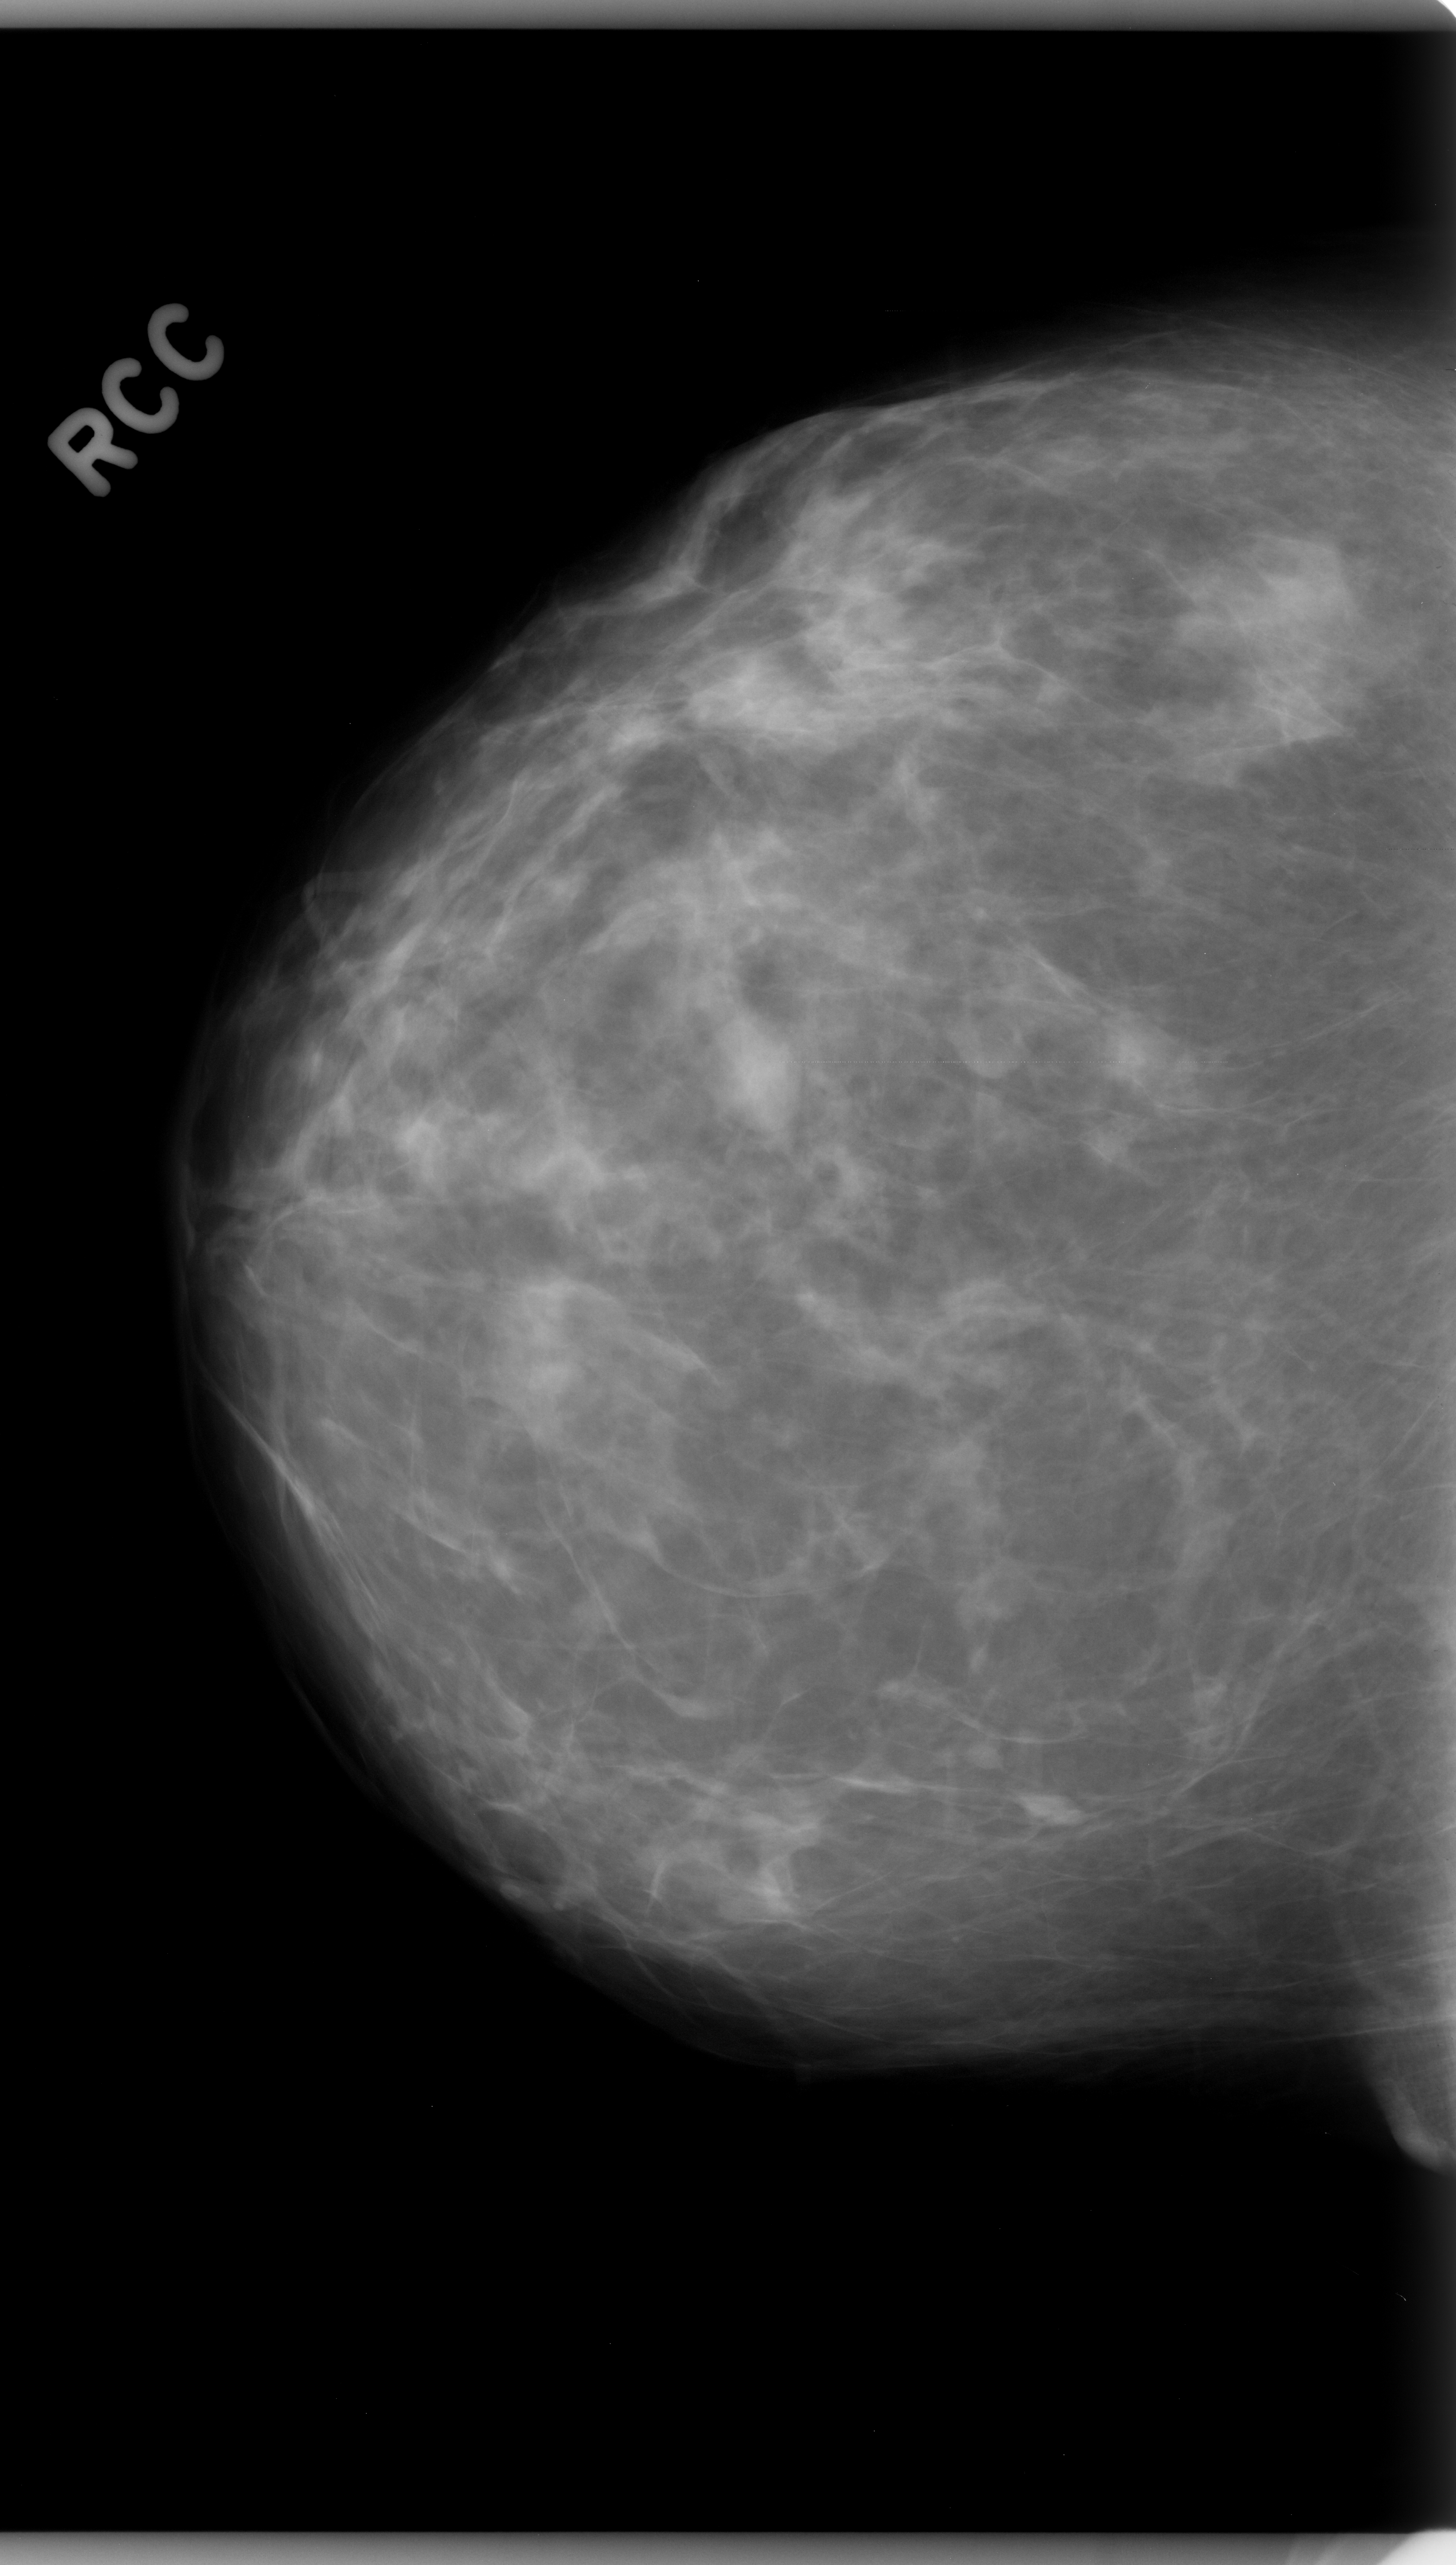
Mammogram (digitized film); right breast; CC view; breast composition: scattered fibroglandular densities (BI-RADS density category 2 of 4); 1456 × 2565 image matrix.
Expert-marked regions of interest on this film, with their recorded descriptors:
- mass, shape oval, margins obscured; BI-RADS assessment category 3; pathology result (as recorded, not read from the image): benign: bounding box <479,1268,593,1431> (left, top, right, bottom; pixels)